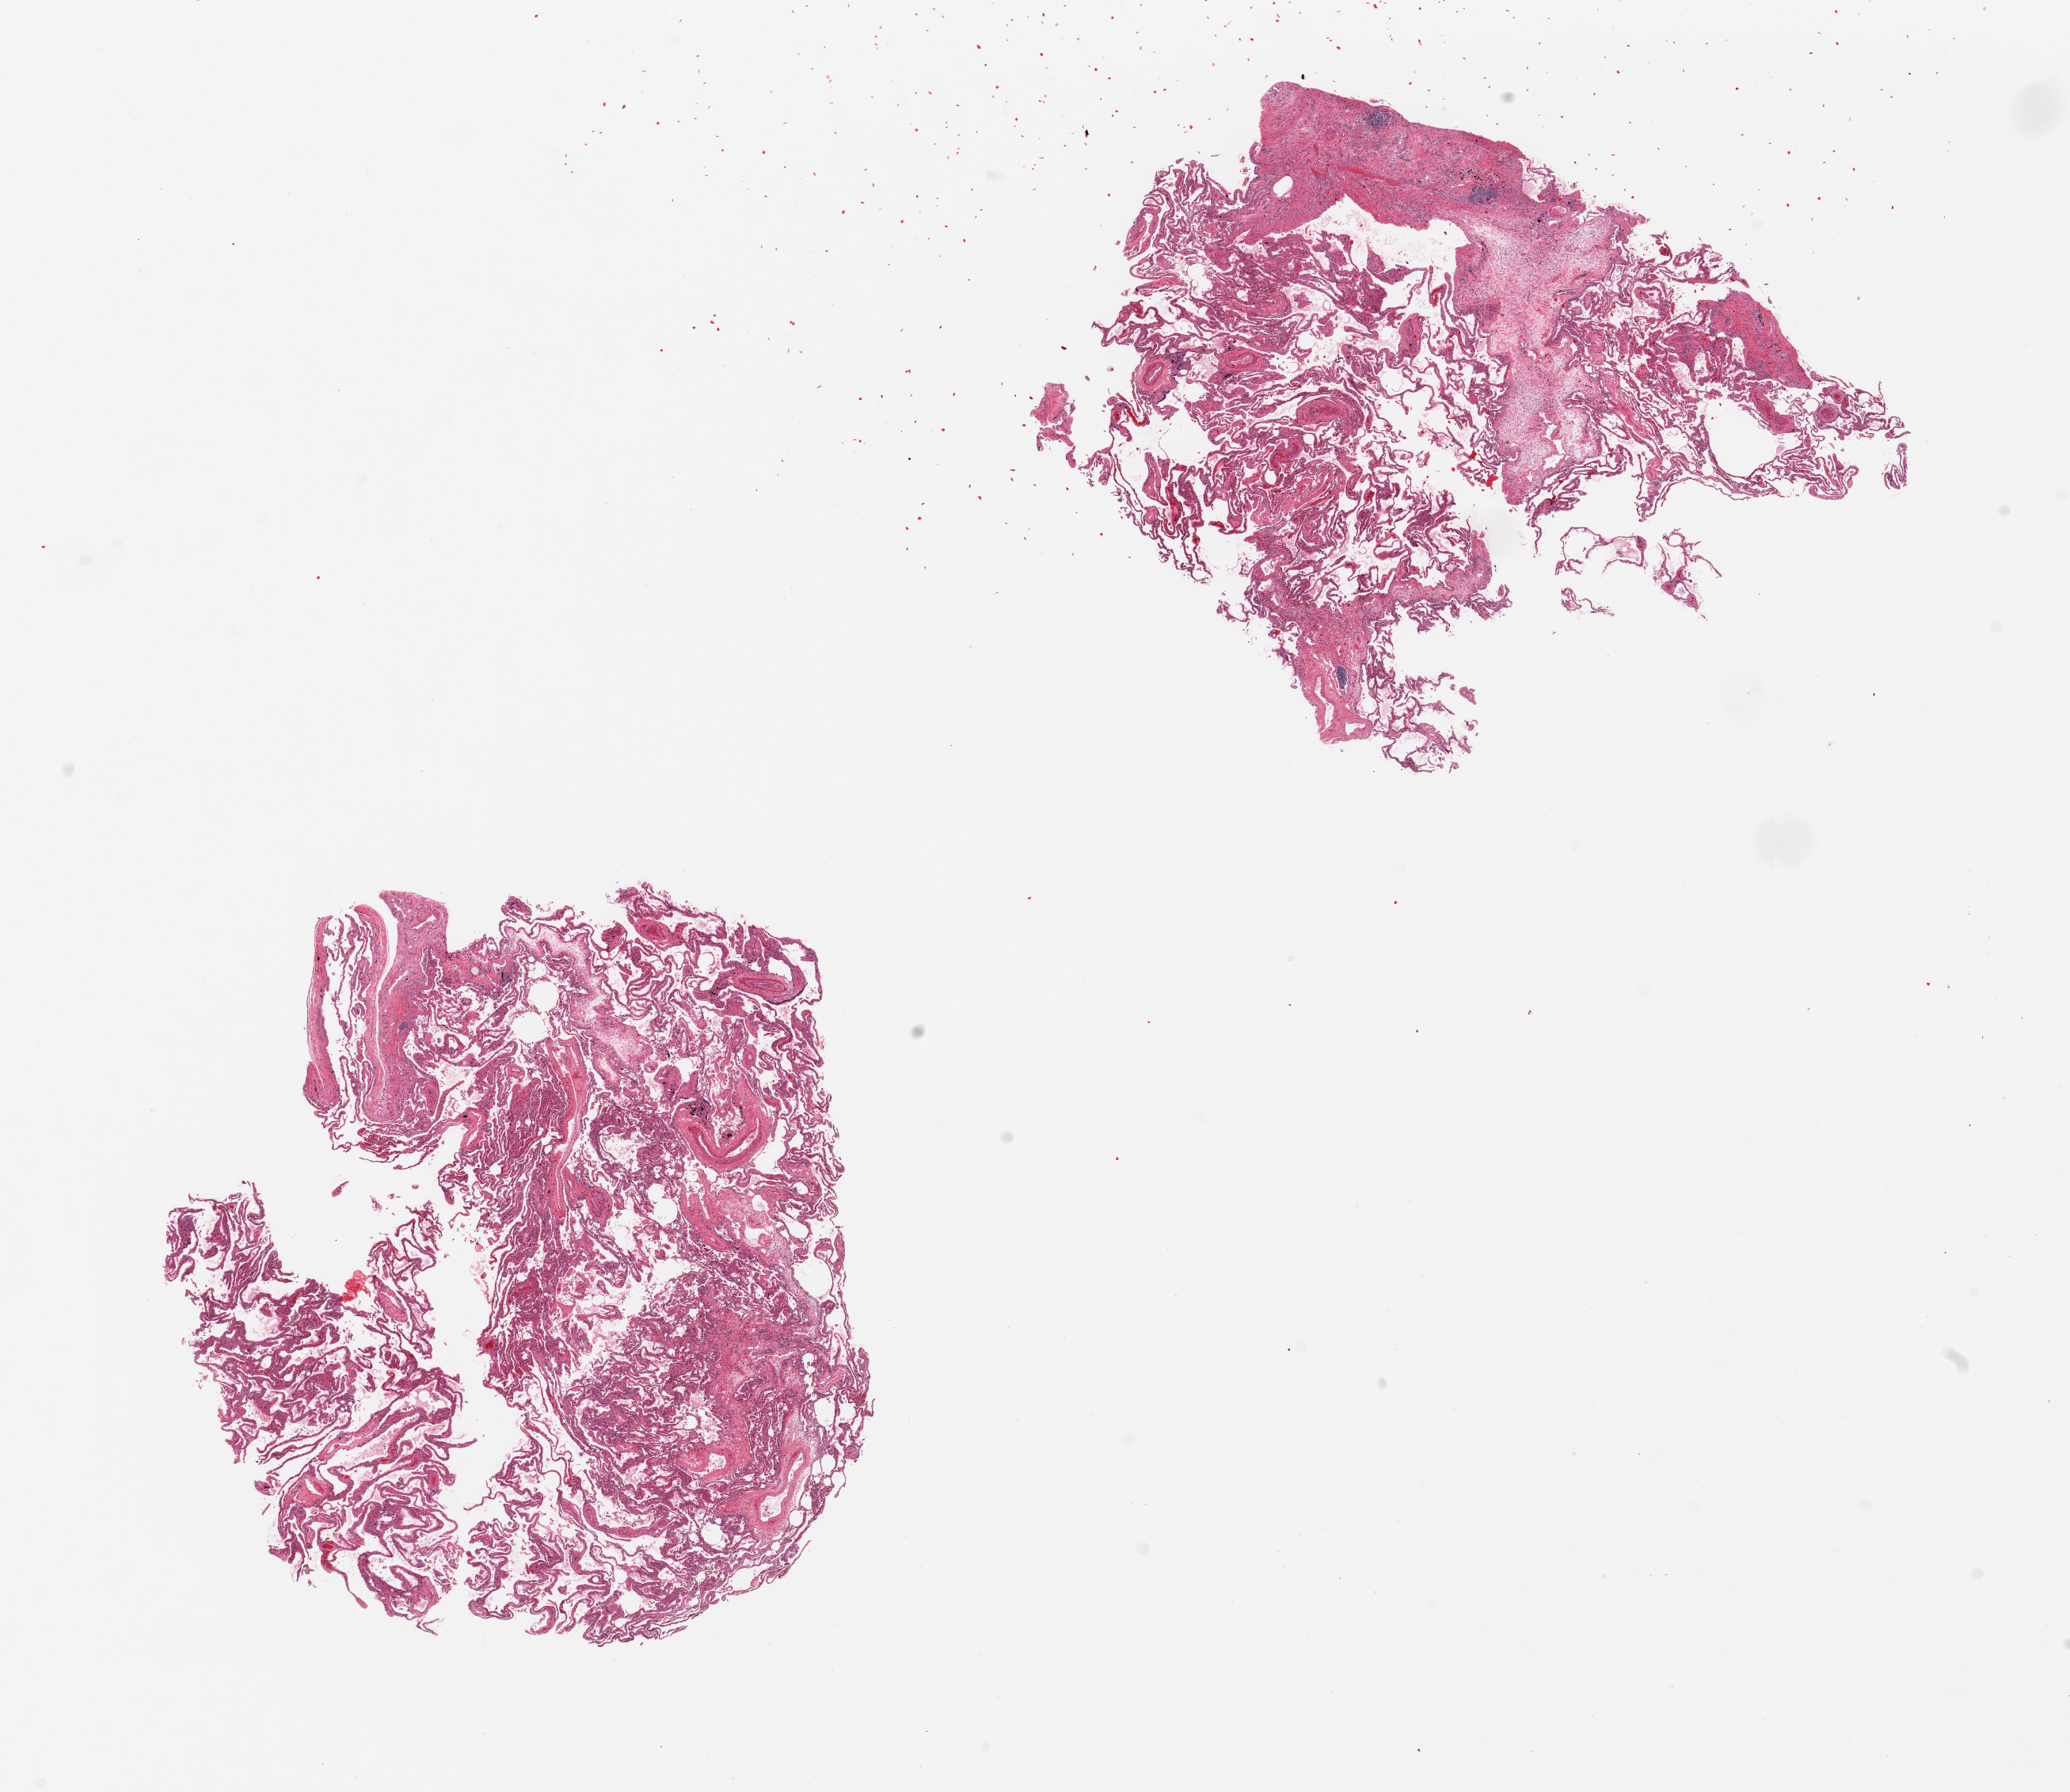
Whole-slide image, hematoxylin and eosin (H&E) stain — low-resolution overview of the scanned area, about 20.7 x 17.9 mm. PAXgene-fixed, paraffin-embedded tissue. Section of lung (target tissue). Tissue donor sample. Donor sex: male.
Reviewer comment on this tissue sample: 2 pieces, moderate congestion2.